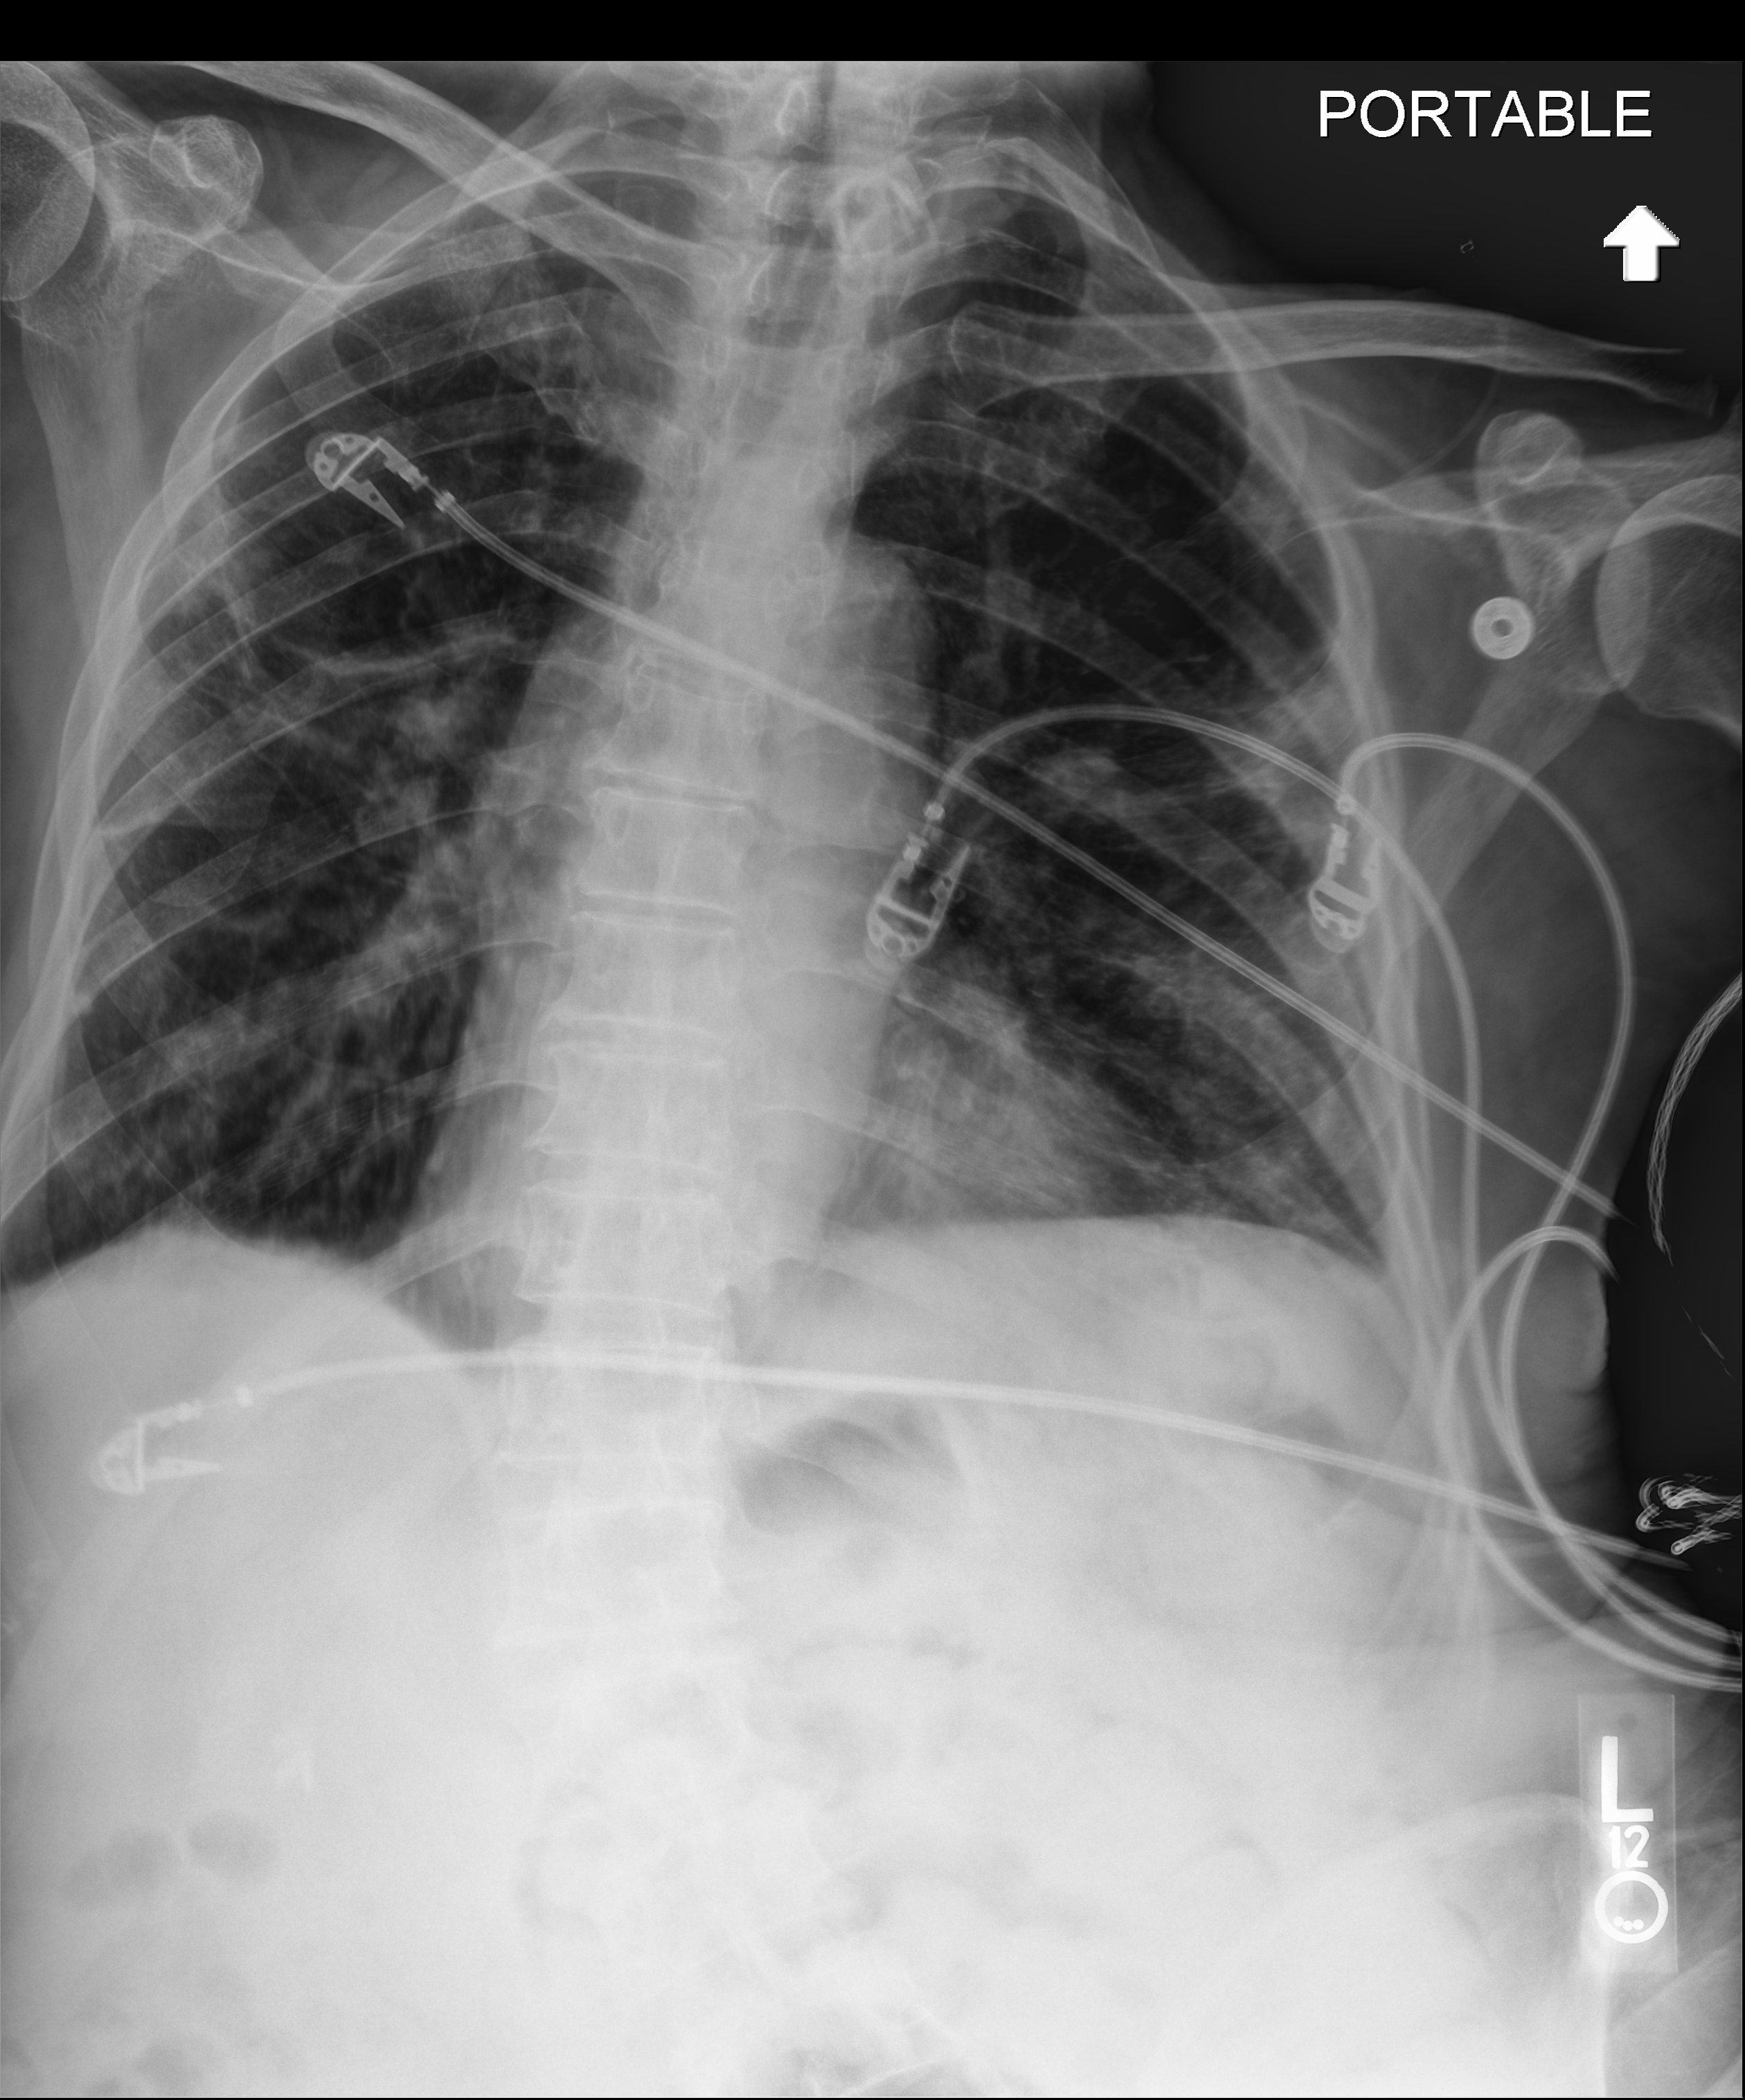
Abdomen X-ray. Male patient hospitalised with COVID-19, age 75–90 years.
Admission-level facts for this patient (not findings on this image; timing relative to this image not recorded): diabetes (admission record): no.